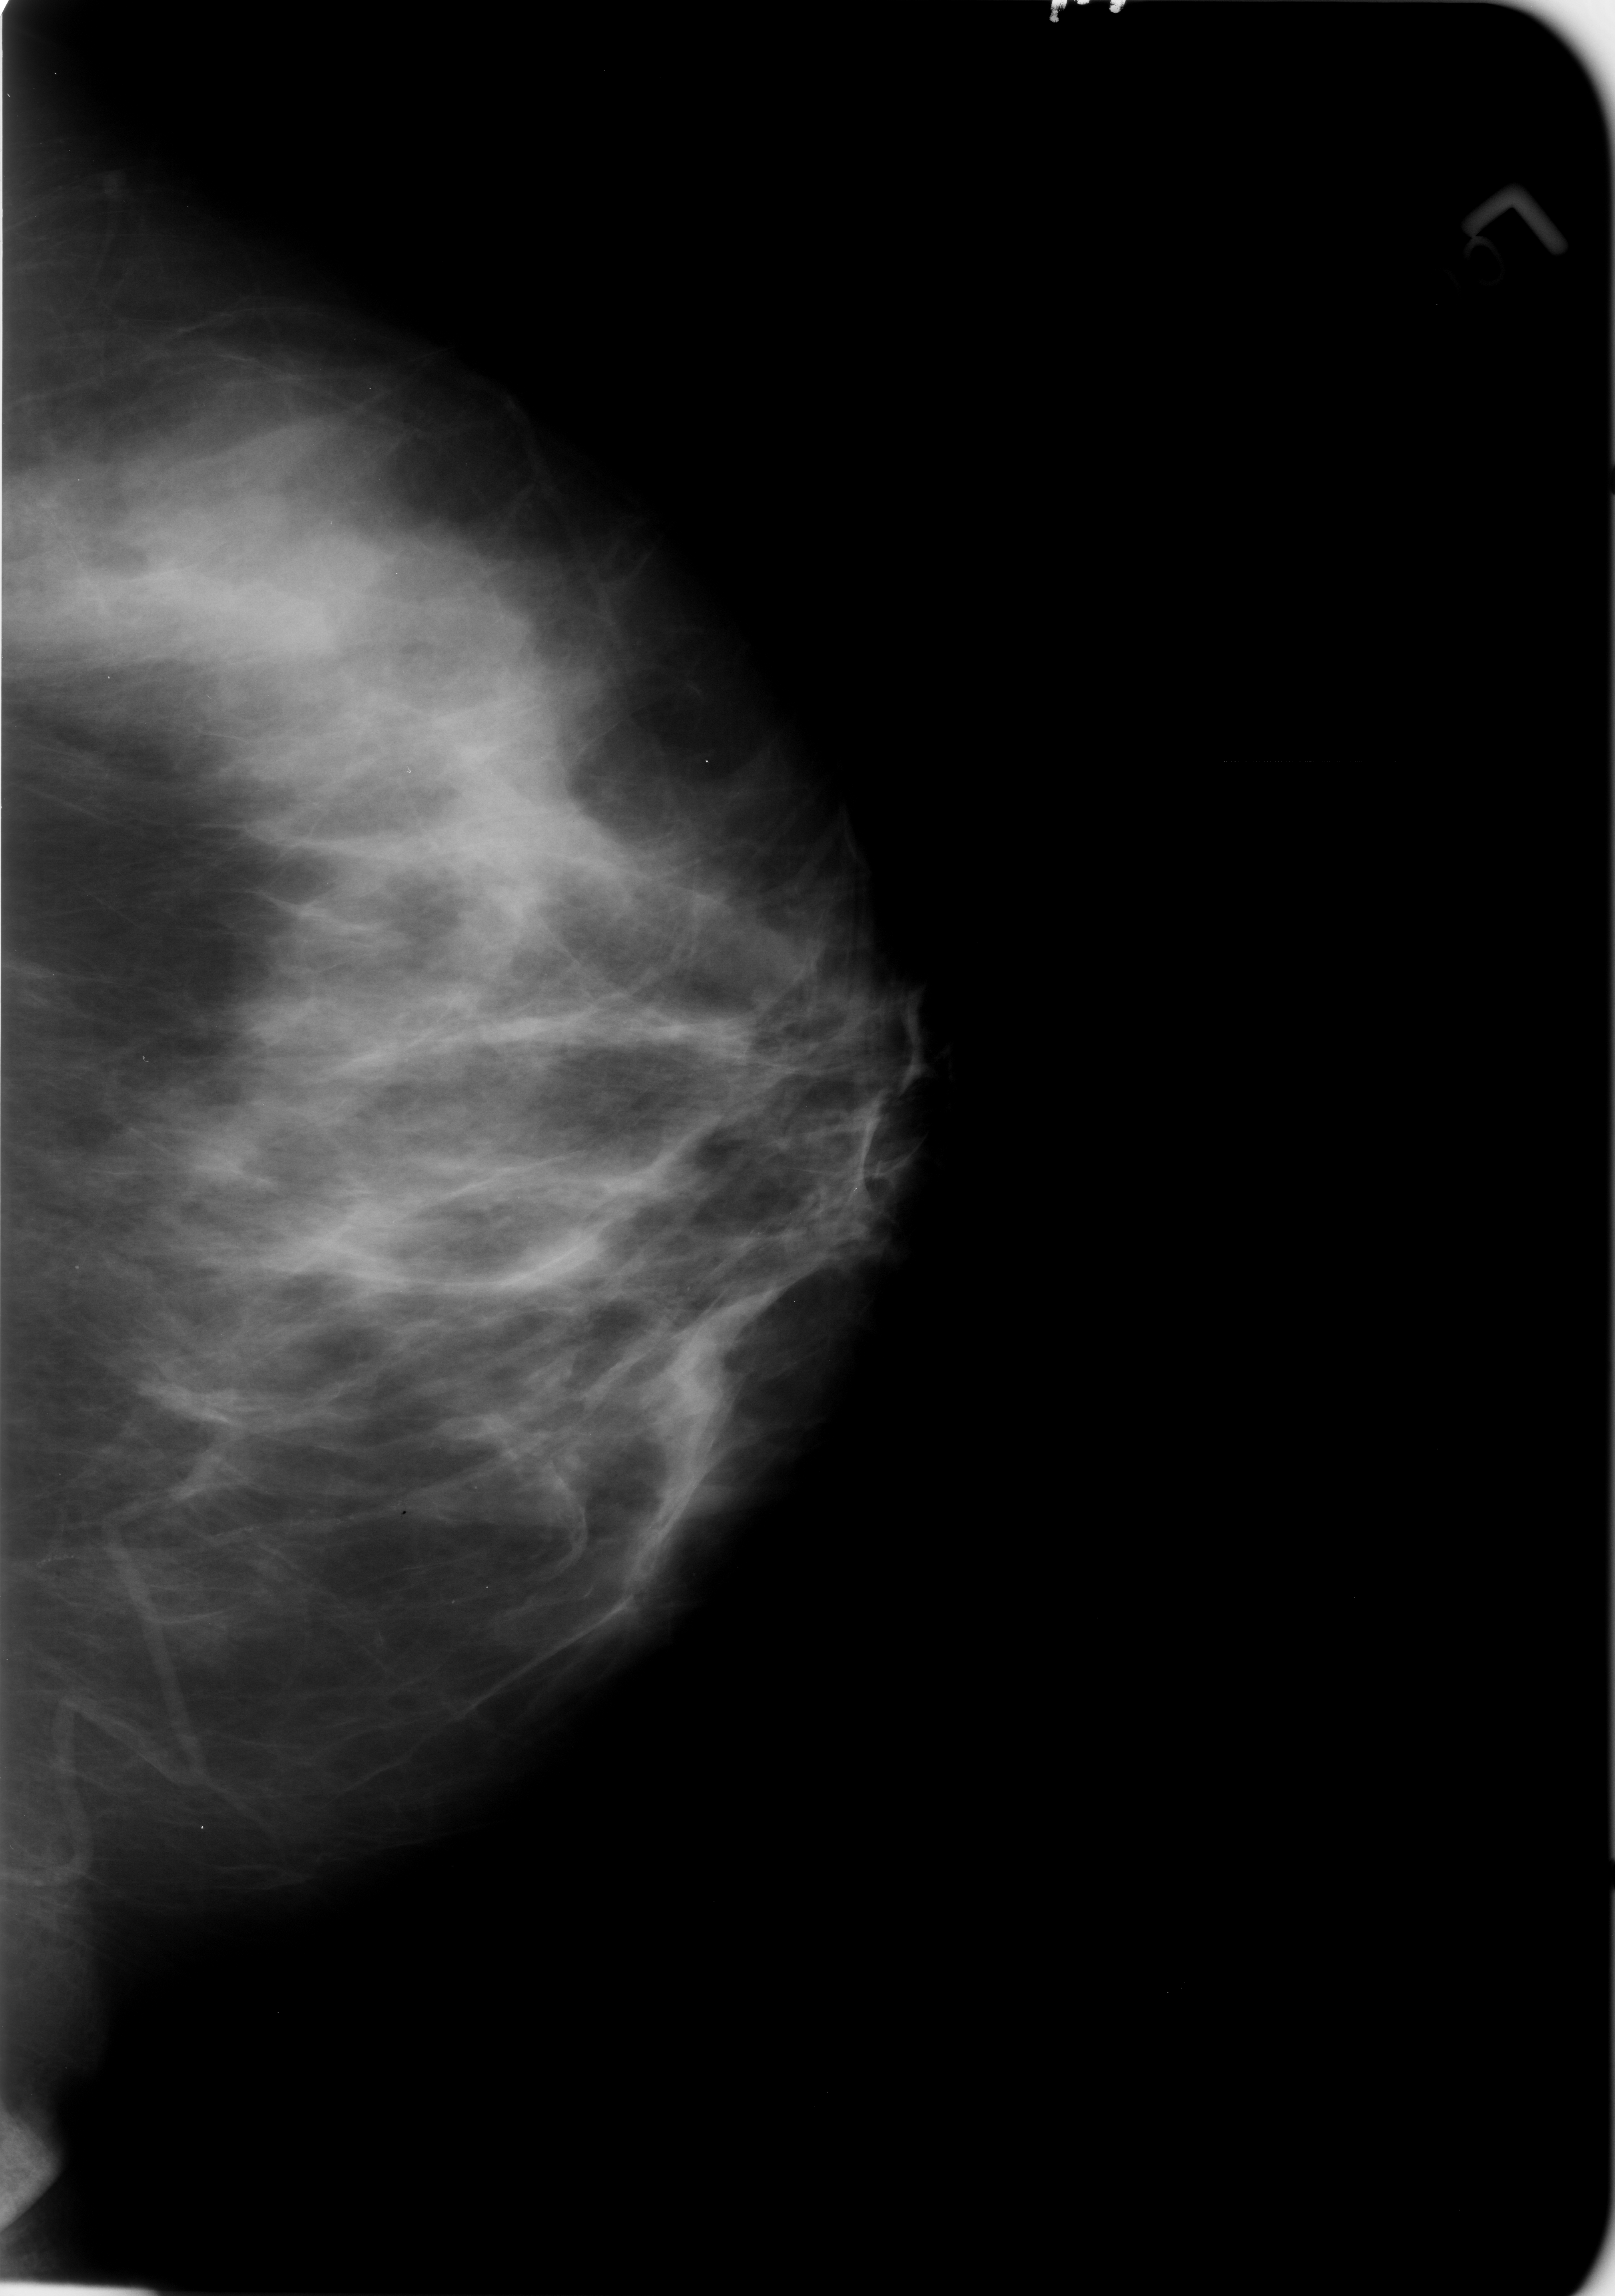
Mammogram (digitized film); left breast; craniocaudal (CC) view; breast composition: heterogeneously dense (BI-RADS density category 3 of 4); 1615 × 2296 image matrix.
Expert-marked regions of interest on this image (one box per marked abnormality):
- calcifications, morphology vascular; BI-RADS assessment category 2; subtlety rating 3 on a 1 (subtle) to 5 (obvious) scale; outcome (as recorded, no biopsy): benign without callback (not worked up further): bounding box (x1, y1, x2, y2) in pixels: (92, 1413, 583, 1571)